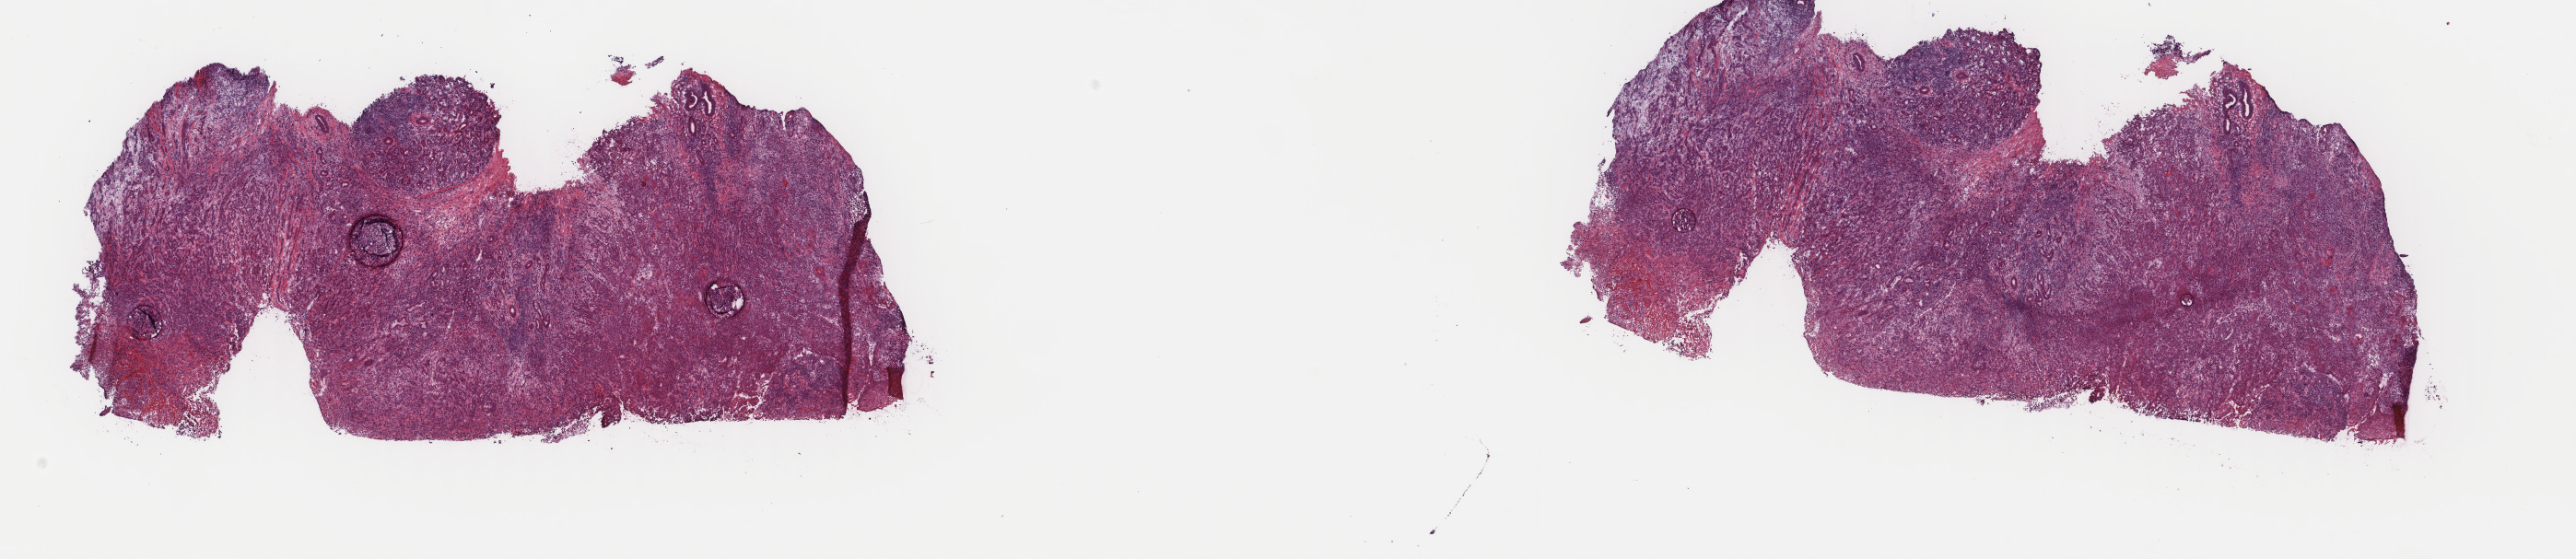
Whole-slide histology image, Hematoxylin and eosin (H&E) stained, whole scanned area (about 22.2 x 4.8 mm) shown as a low-resolution overview; frozen section from the top of the tissue portion; head and neck, primary tumour sample. Male patient; age at initial diagnosis 44 years. Histologic grade: G2 (moderately differentiated). Composition of this section per pathologist review: tumour cells 65%, tumour nuclei 65%, normal cells 5%, stromal cells 30%, necrosis 0%. Inflammatory infiltration, as recorded: lymphocyte infiltration 5%, monocyte infiltration 2%, neutrophil infiltration 4%.
Pathologic diagnosis: Squamous cell carcinoma, keratinizing, NOS. Lymph nodes positive (case pathology): 5 of 42 examined. AJCC pathologic stage: IVA. TNM: T4a N2c M0.